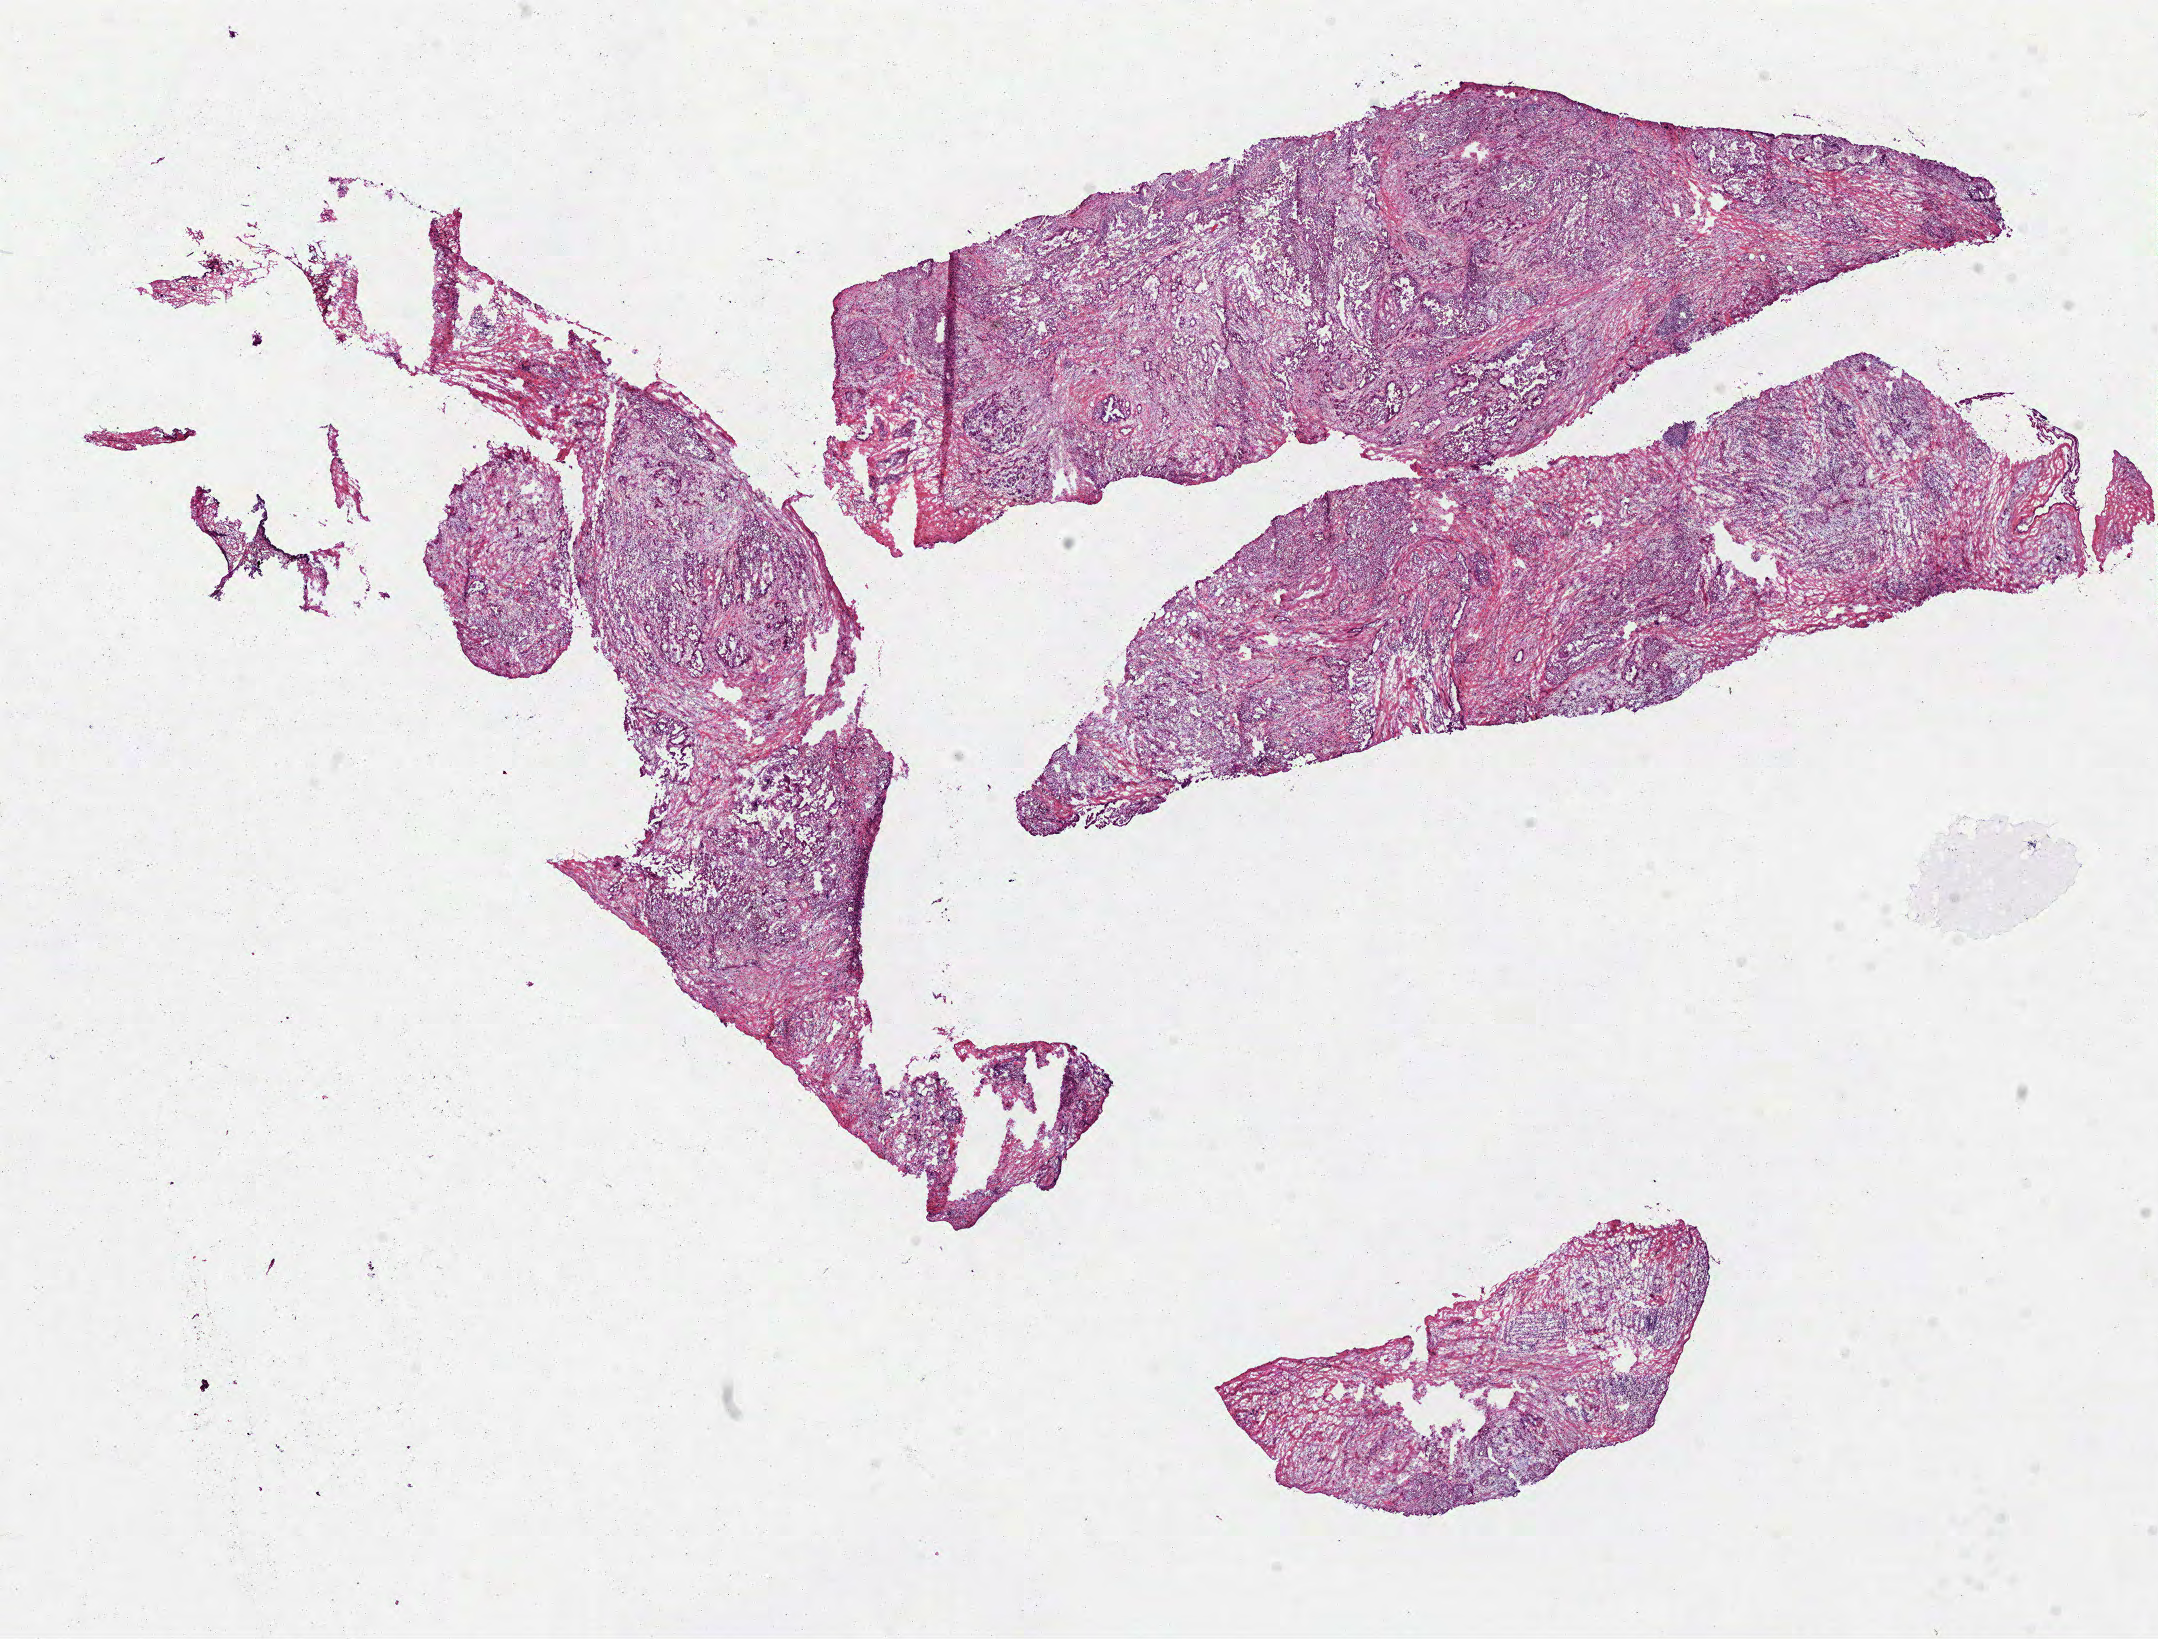
Hematoxylin and eosin (H&E) stained whole-slide image — whole scanned area (about 17.4 x 13.2 mm, from a 40x scan) shown as a low-resolution overview. Frozen section from the bottom of the tissue portion. Pancreas, primary tumour sample. Female, age 79 years at initial diagnosis. Histologic grade: G1 (well differentiated). Composition of this section per pathologist review: tumour cells 90%, tumour nuclei 61%, normal cells 0%, stromal cells 10%, necrosis 0%. Infiltration values recorded for this section: lymphocyte infiltration 25%, monocyte infiltration 0%, neutrophil infiltration 10%.
Lymph nodes positive (case pathology): 5 of 10 examined. Diagnosis: Infiltrating duct carcinoma, NOS (head of pancreas). AJCC pathologic stage: III.